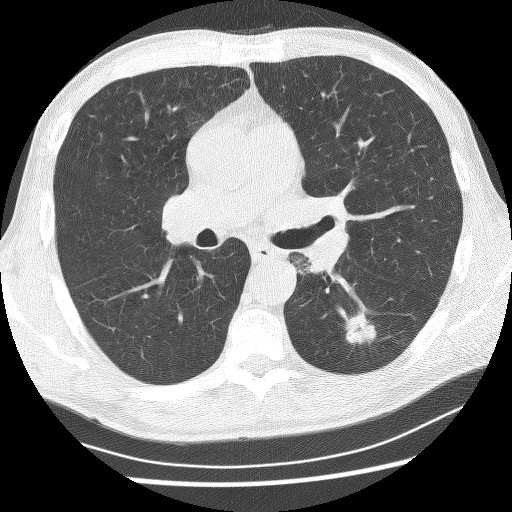
Axial slice from a low-dose chest CT screening exam. First (baseline) screen. Lung window (W 1500 / L -600 HU). Lung (sharp) reconstruction kernel (BONE). 120 kVp. Slice 110 of 253 in the series. 512 × 512 image matrix. Male, age 62 years at enrolment. Current smoker at enrolment.
Expert-annotated lung lesion, bounding box [x1, y1, x2, y2] px = [329, 306, 383, 351]. The exam's reader record, not a measurement of the box and not confirmed to be the same lesion: non-calcified nodule or mass ≥4 mm, left lower lobe, 21 × 17 mm, spiculated (stellate) margins, soft tissue attenuation. Participant outcome: lung cancer diagnosed 58 days after this screen — non-small cell carcinoma, left lower lobe, poorly differentiated (G3), stage IA (AJCC 6th edition), 11 mm at pathology.